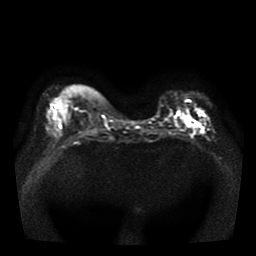
Breast MRI, one axial slice; slice 13 of 41 in the series (ordered by position); diffusion-weighted series; image 2 of 4 stored at this slice position (different b-values; order by instance number); 1.5 T; 5 mm slice thickness; 256 × 256 image matrix, field of view 330 × 330 mm. Female patient.
Outlined on this slice (manually delineated by an expert):
- tumour on diffusion-weighted imaging: bounding box [x1, y1, x2, y2] px = [188, 119, 199, 128]